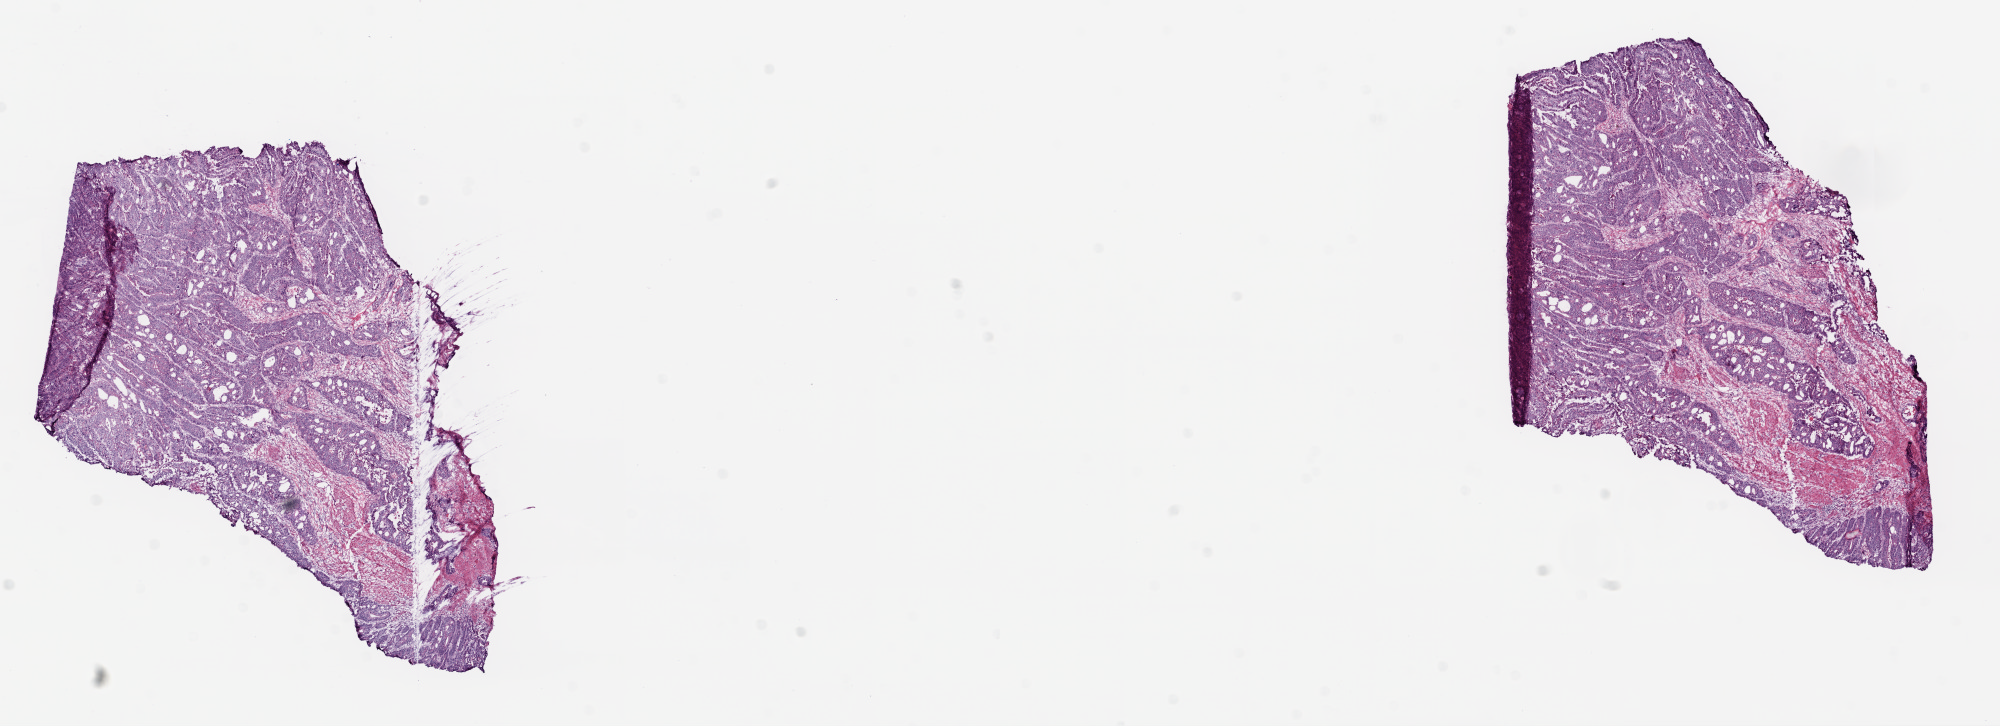
Digitized Hematoxylin and eosin (H&E) stained tissue section (whole slide), shown as a low-resolution overview of the whole scanned area (about 16.0 x 5.8 mm, from a 20x scan), frozen section from the top of the tissue portion, sample: primary tumour, colon. Female, age 84 years at initial diagnosis. Pathologist review of this section (percent, as recorded): tumour cells 70%, tumour nuclei 80%, normal cells 10%, stromal cells 15%, necrosis 5%.
• lymph nodes positive (case pathology): 3 of 41 examined
• AJCC pathologic stage: IVA
• diagnosis: Adenocarcinoma, NOS